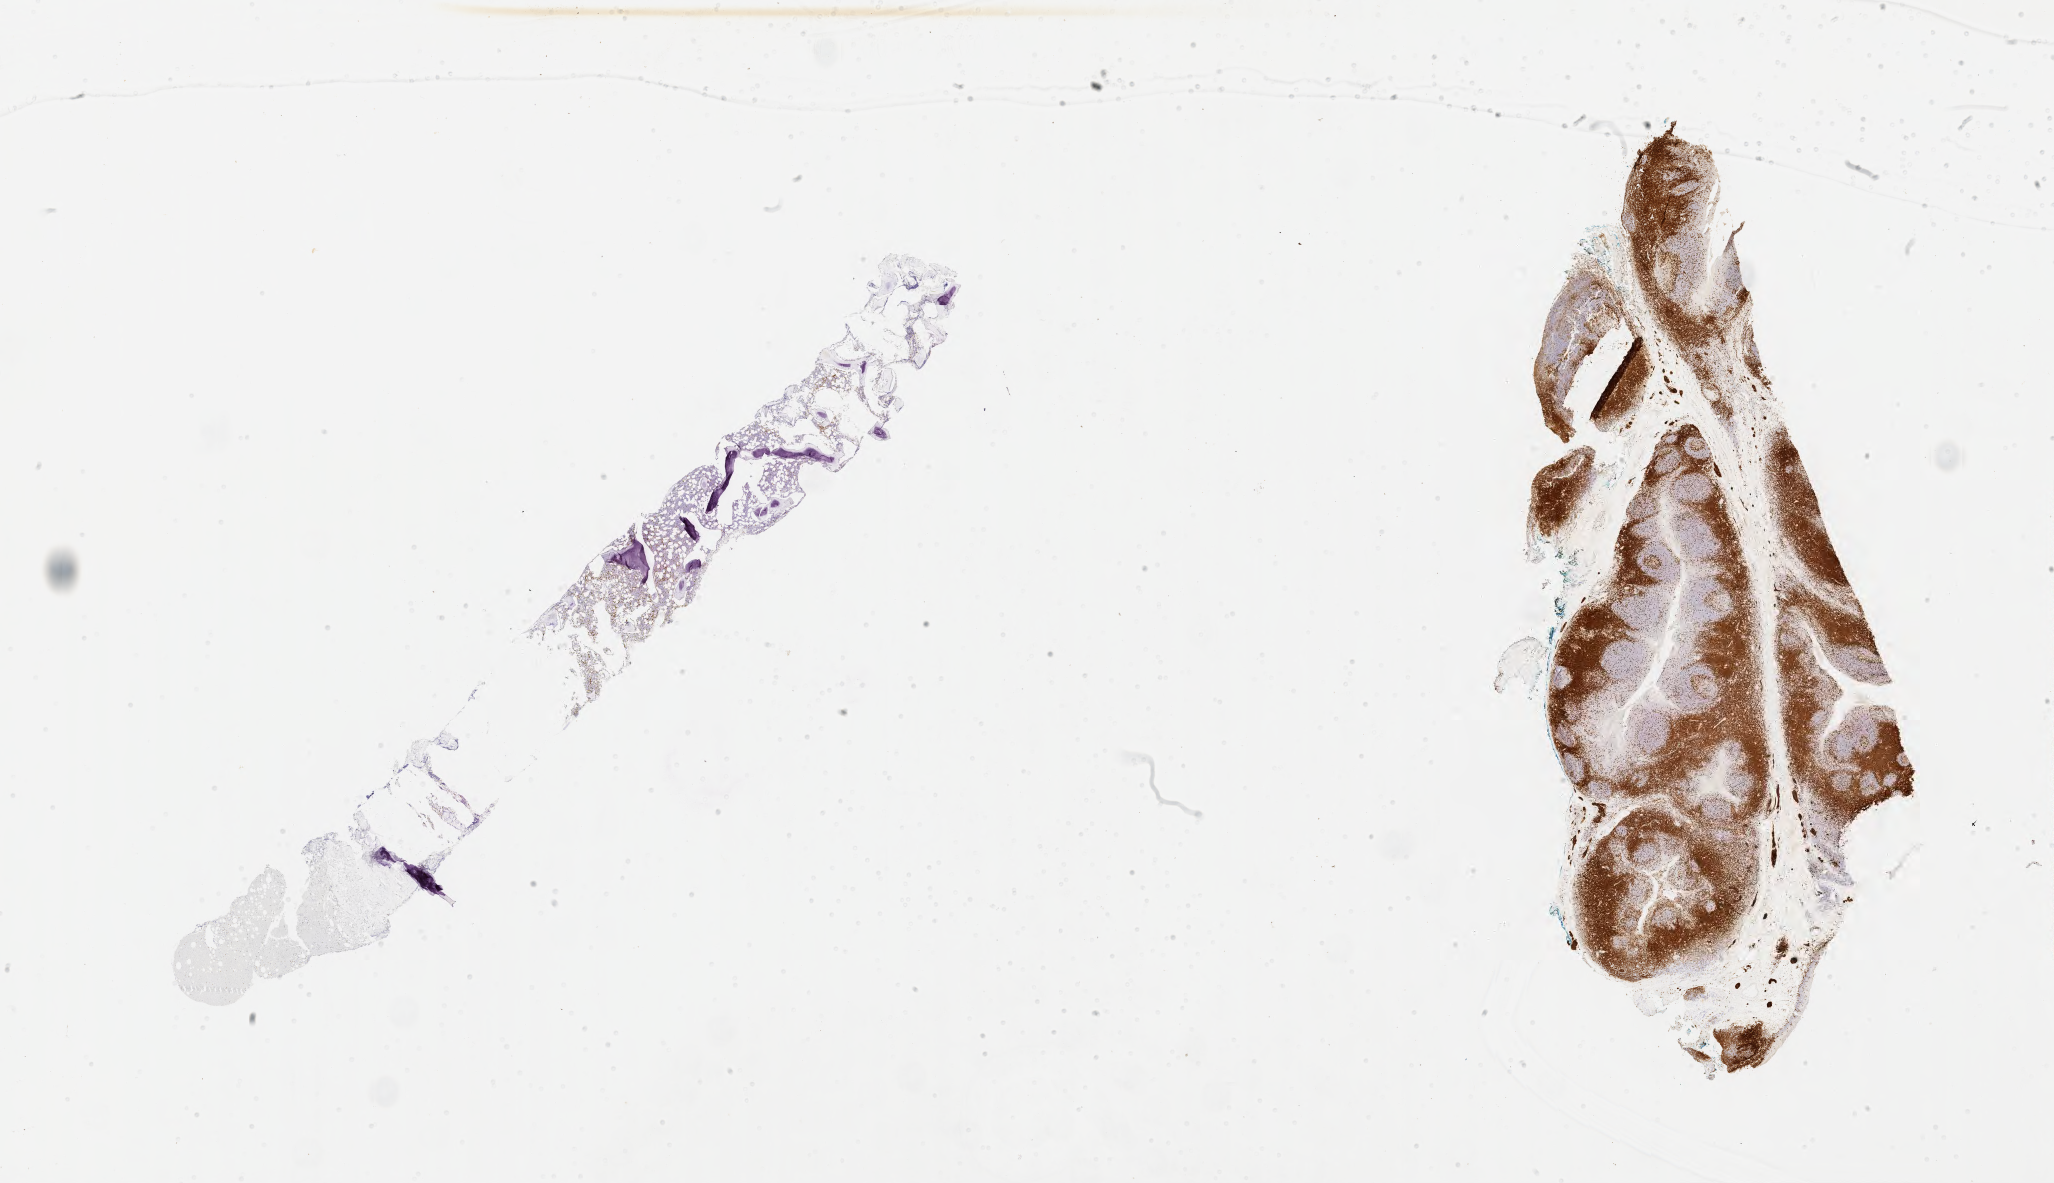
IHC for CD3, whole-slide image — low-resolution overview of the scanned area, about 33.2 x 19.1 mm, tumor tissue, site: bone marrow. Patient male; age 15 years.
Histologic diagnosis: Burkitt lymphoma, NOS.